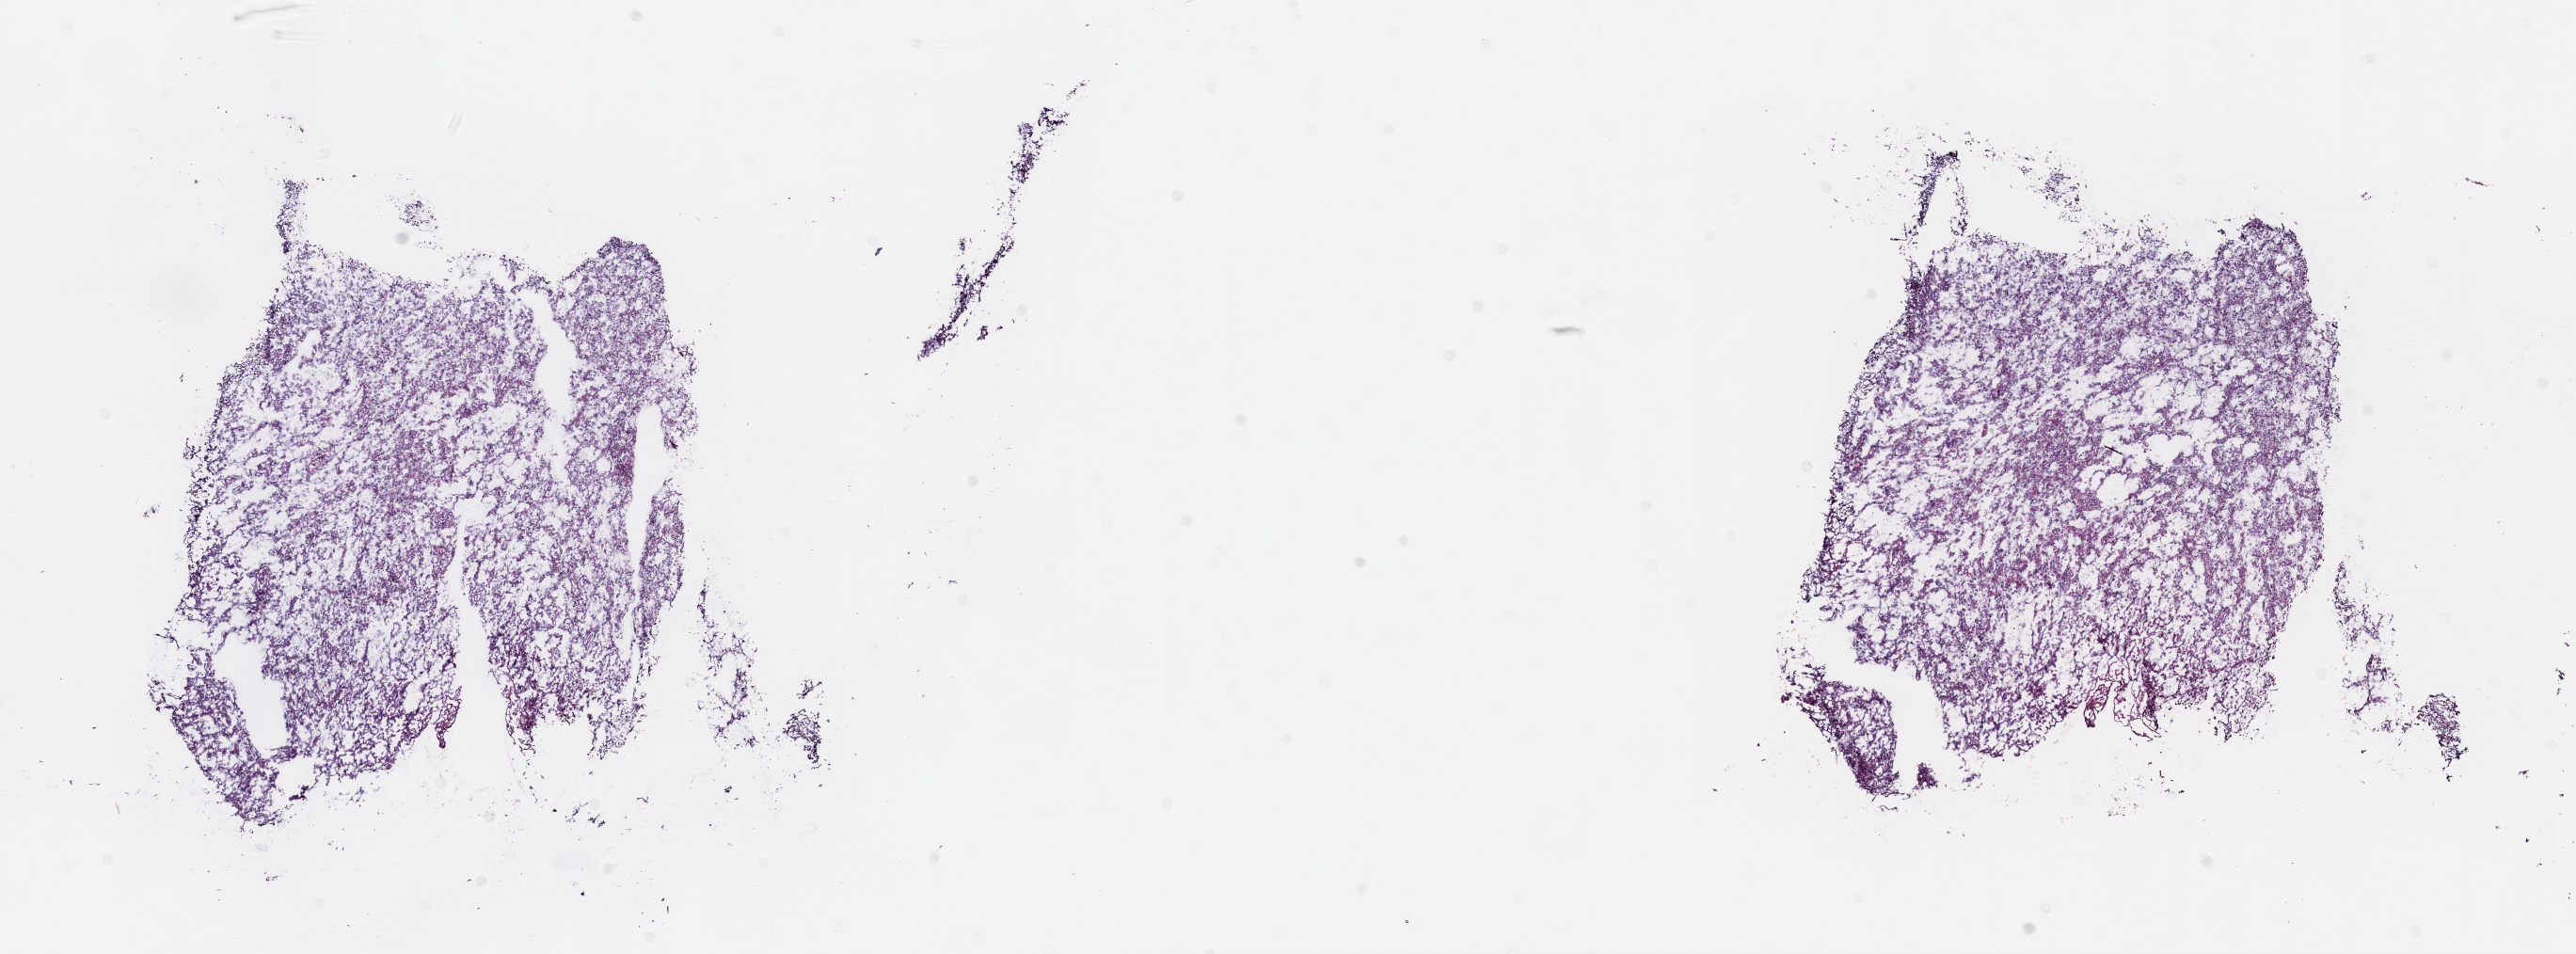
Digitized H&E tissue section (whole slide) — a low-resolution overview of the entire scanned area, about 22.1 x 8.2 mm (acquisition: 40x scan). Frozen section from the top of the tissue portion. Brain, primary tumour sample. Male patient; age at initial diagnosis 36 years. Histologic grade: G2 (moderately differentiated). Pathologist review of this section (percent, as recorded): tumour cells 45%, tumour nuclei 90%, normal cells 10%, stromal cells 45%, necrosis 0%. Infiltration values recorded for this section: lymphocyte infiltration 0%, monocyte infiltration 0%, neutrophil infiltration 0%.
Diagnosis: Astrocytoma, NOS (cerebrum). Laterality: right.